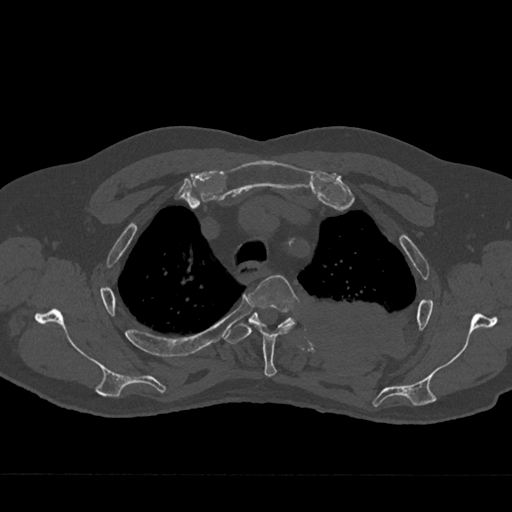
CT including the spine, one axial slice. Position 547 of 797 along the scan axis. Reconstruction kernel Br40s/3. 120 kVp. Bone window (W 1800 / L 400 HU). 512 × 512 image matrix, field of view 377 × 377 mm. Male patient, age 75 years. From the clinical record (not read from this slice): primary cancer: renal; vertebrae with lytic lesions (as recorded): T4.
Outlined on this slice (semi-automatic segmentation, software-assisted and operator-edited):
- T3 vertebra: box from (x=249, y=275) to (x=300, y=377) px
- T4 vertebra: (x=225, y=312)–(x=296, y=344)